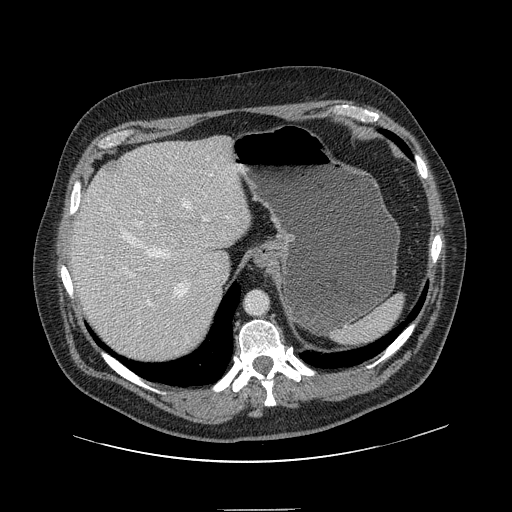
Contrast-enhanced abdominal CT, one axial slice; slice 113 of 154 in the series (ordered by position); intravenous contrast given; soft-tissue window (W 400 / L 40 HU); 2.5 mm slice thickness; 512 × 512 image matrix, field of view 451 × 451 mm. Male patient, age 61 years. Case-level facts recorded for this patient, not image findings: diagnosis: colorectal cancer liver metastases, imaged before liver resection; multiple liver metastases: yes; largest metastasis: 2.6 cm; disease in both lobes: yes.
Structures marked on this image (outlined manually by an expert reader):
- hepatic veins: bounding box [x1, y1, x2, y2] px = [118, 198, 190, 297]
- liver: [71, 138, 250, 364]
- planned liver remnant (the part of the liver to remain after resection): [72, 145, 250, 356]
- portal vein (with intrahepatic branches): [123, 199, 207, 305]